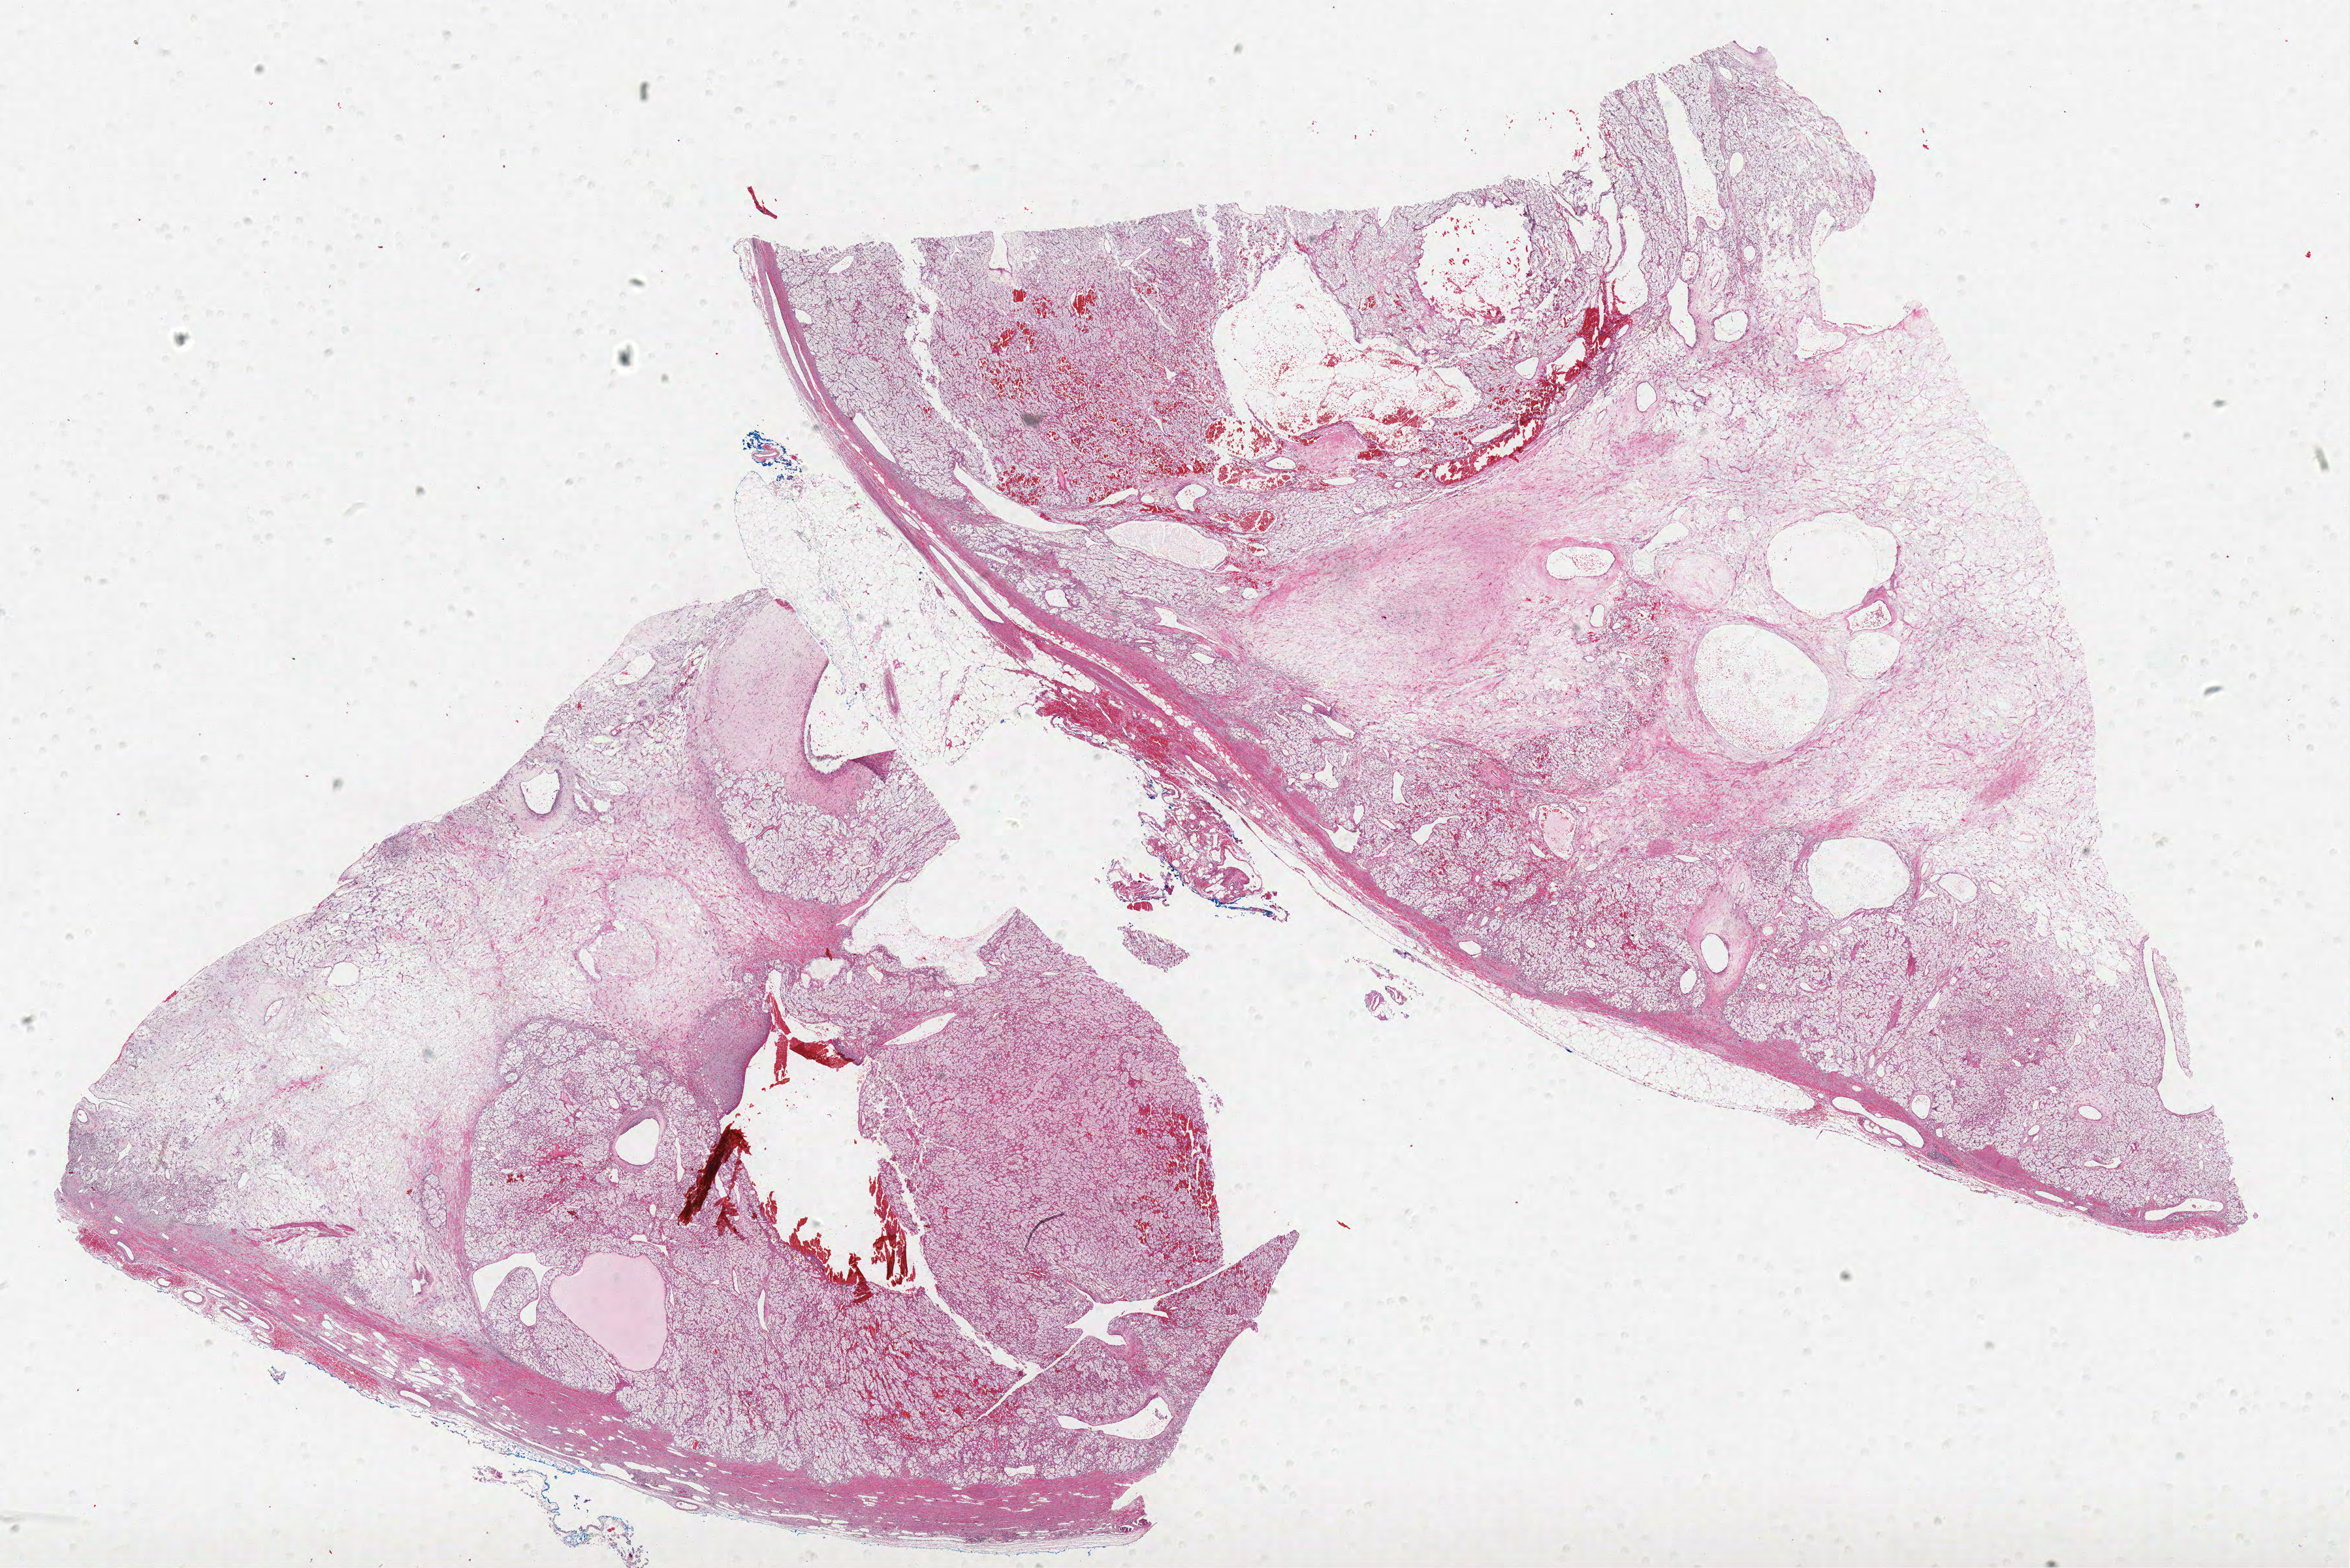
Digitized H&E-stained tissue section (whole slide), low-resolution overview of the scanned area, about 28.8 x 19.2 mm, formalin-fixed paraffin-embedded (FFPE) diagnostic section, kidney, primary tumour sample. Patient: male, age at initial diagnosis 75 years. Histologic grade: G2 (moderately differentiated).
Pathologic diagnosis: Clear cell adenocarcinoma, NOS. AJCC pathologic stage: I.